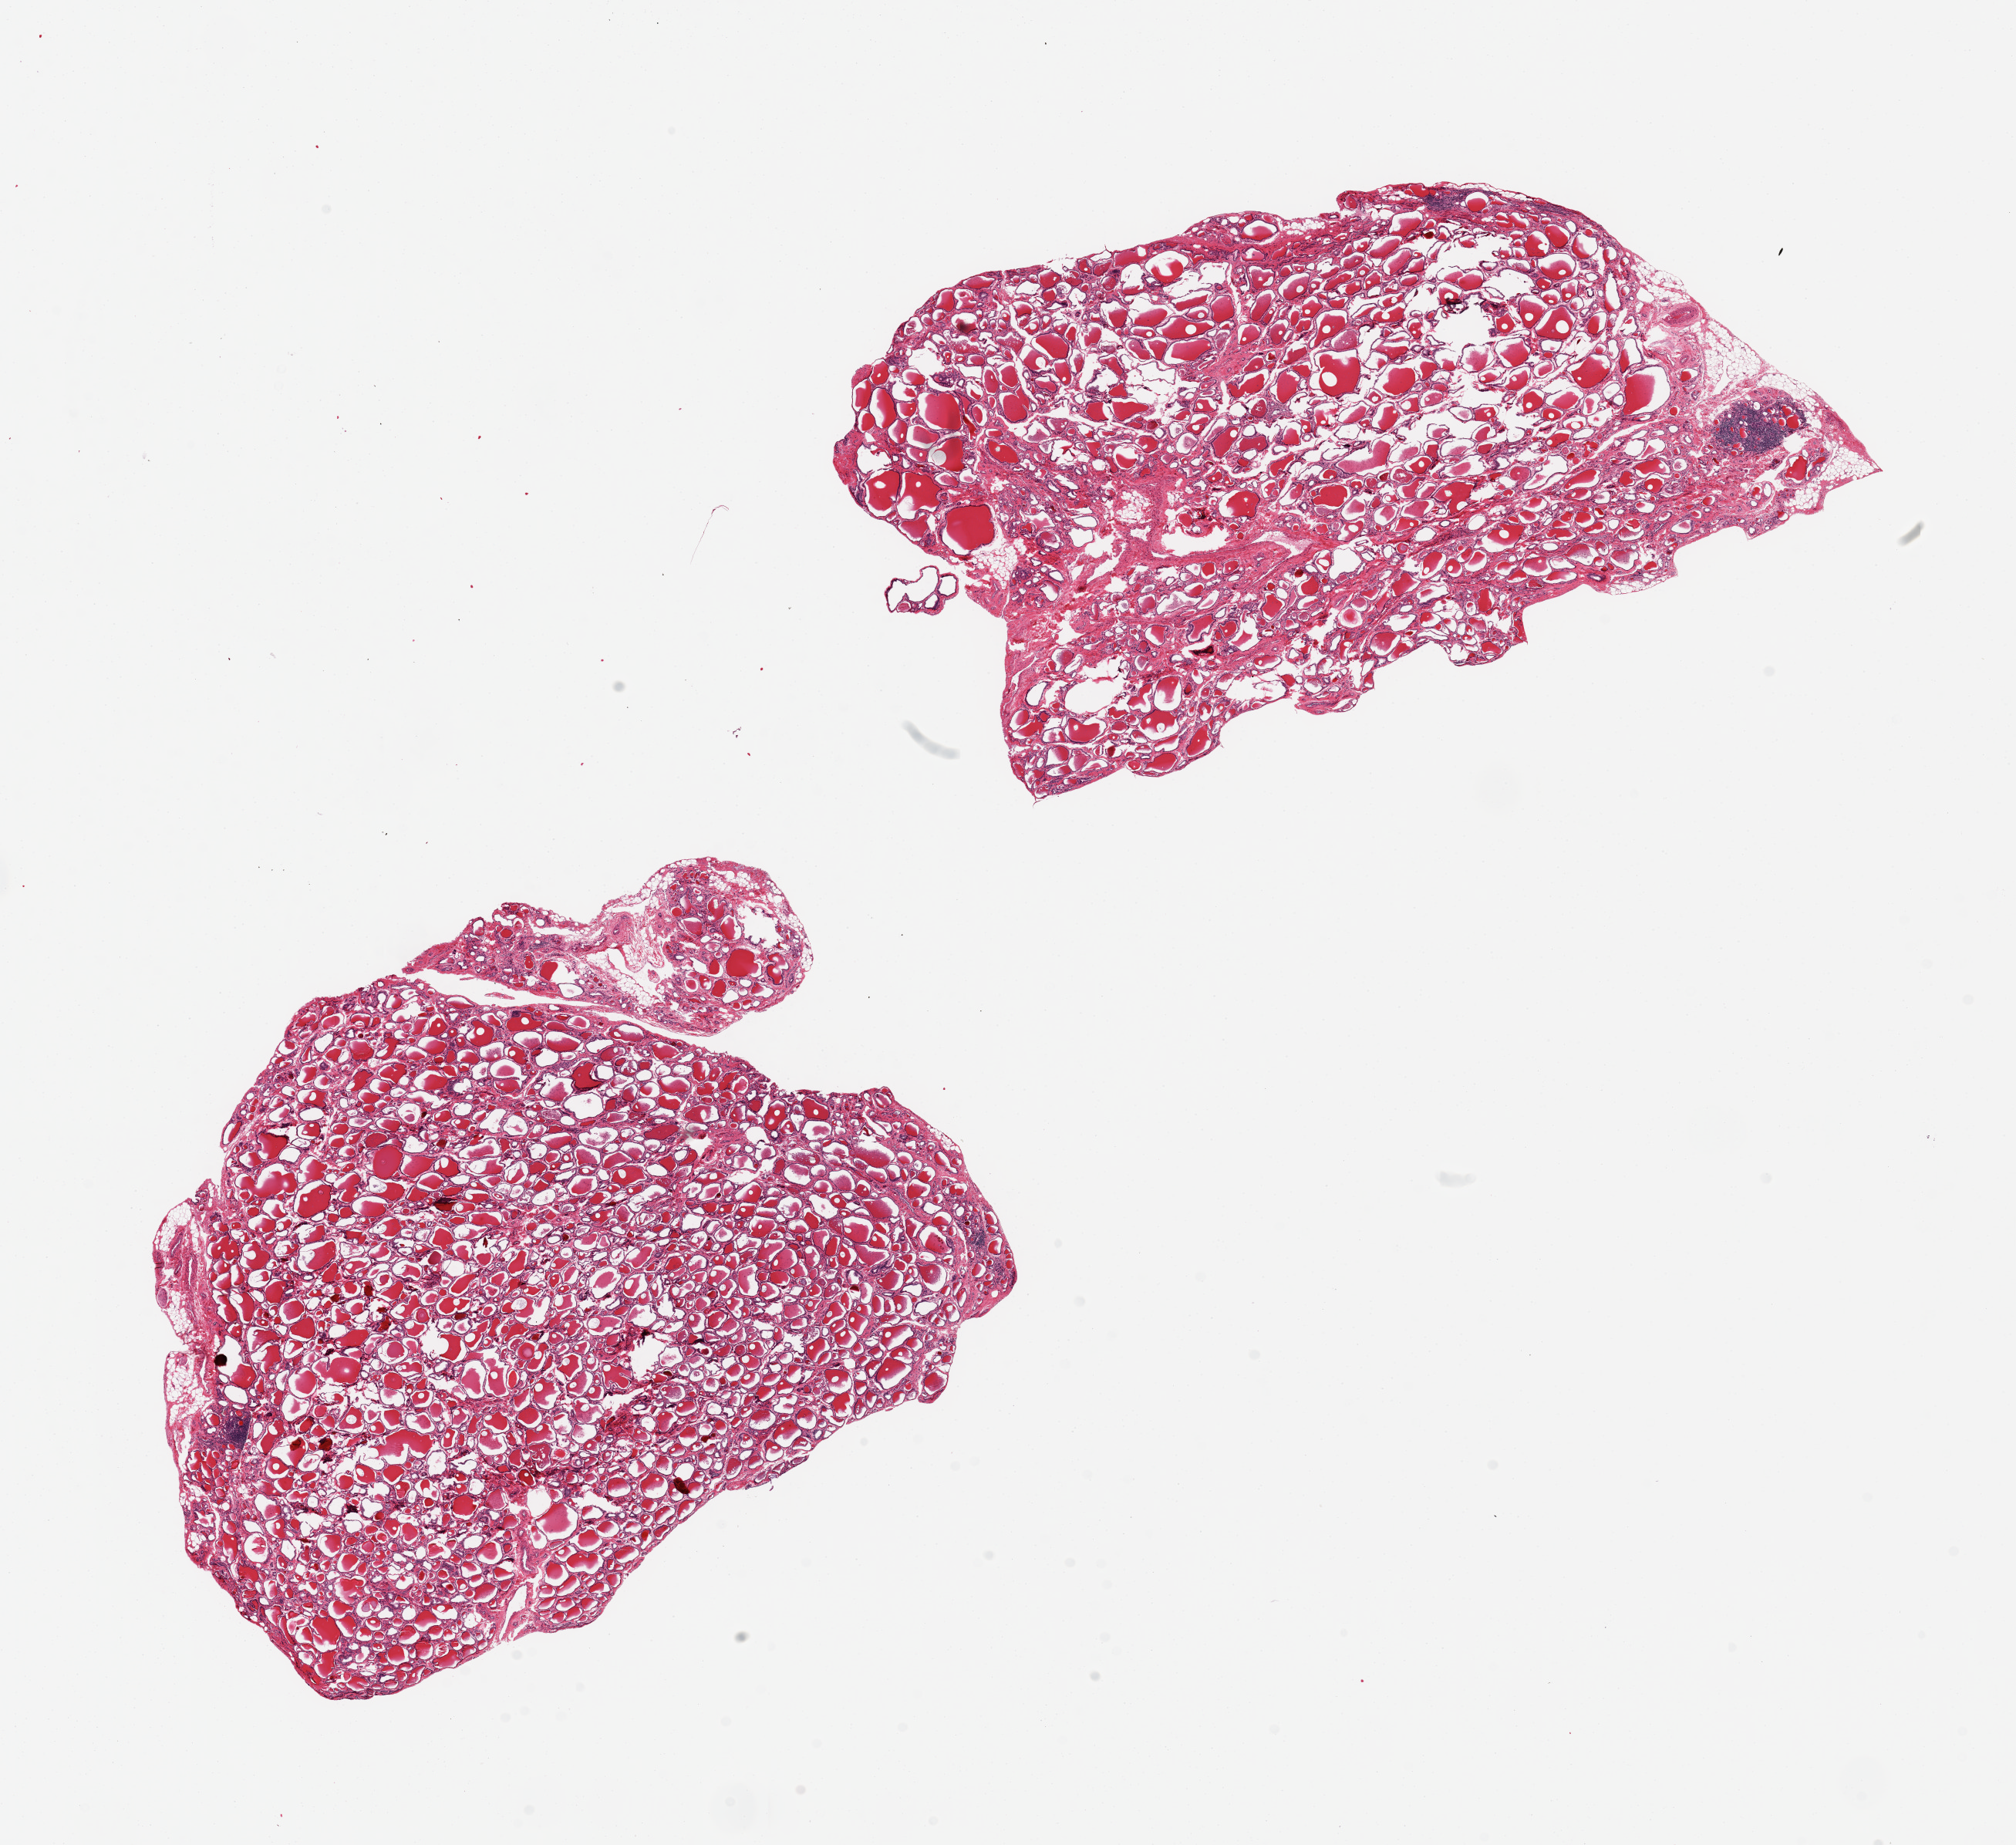
Hematoxylin and eosin (H&E) whole-slide image — shown as a low-resolution overview of the whole scanned area (about 20.7 x 18.9 mm, from a 20x scan), PAXgene-fixed paraffin-embedded (PFPE) section, section of thyroid (target tissue), tissue donor sample.
Pathologist's review note for this sample: 2 pieces, 9x9 & 10x5 mm.